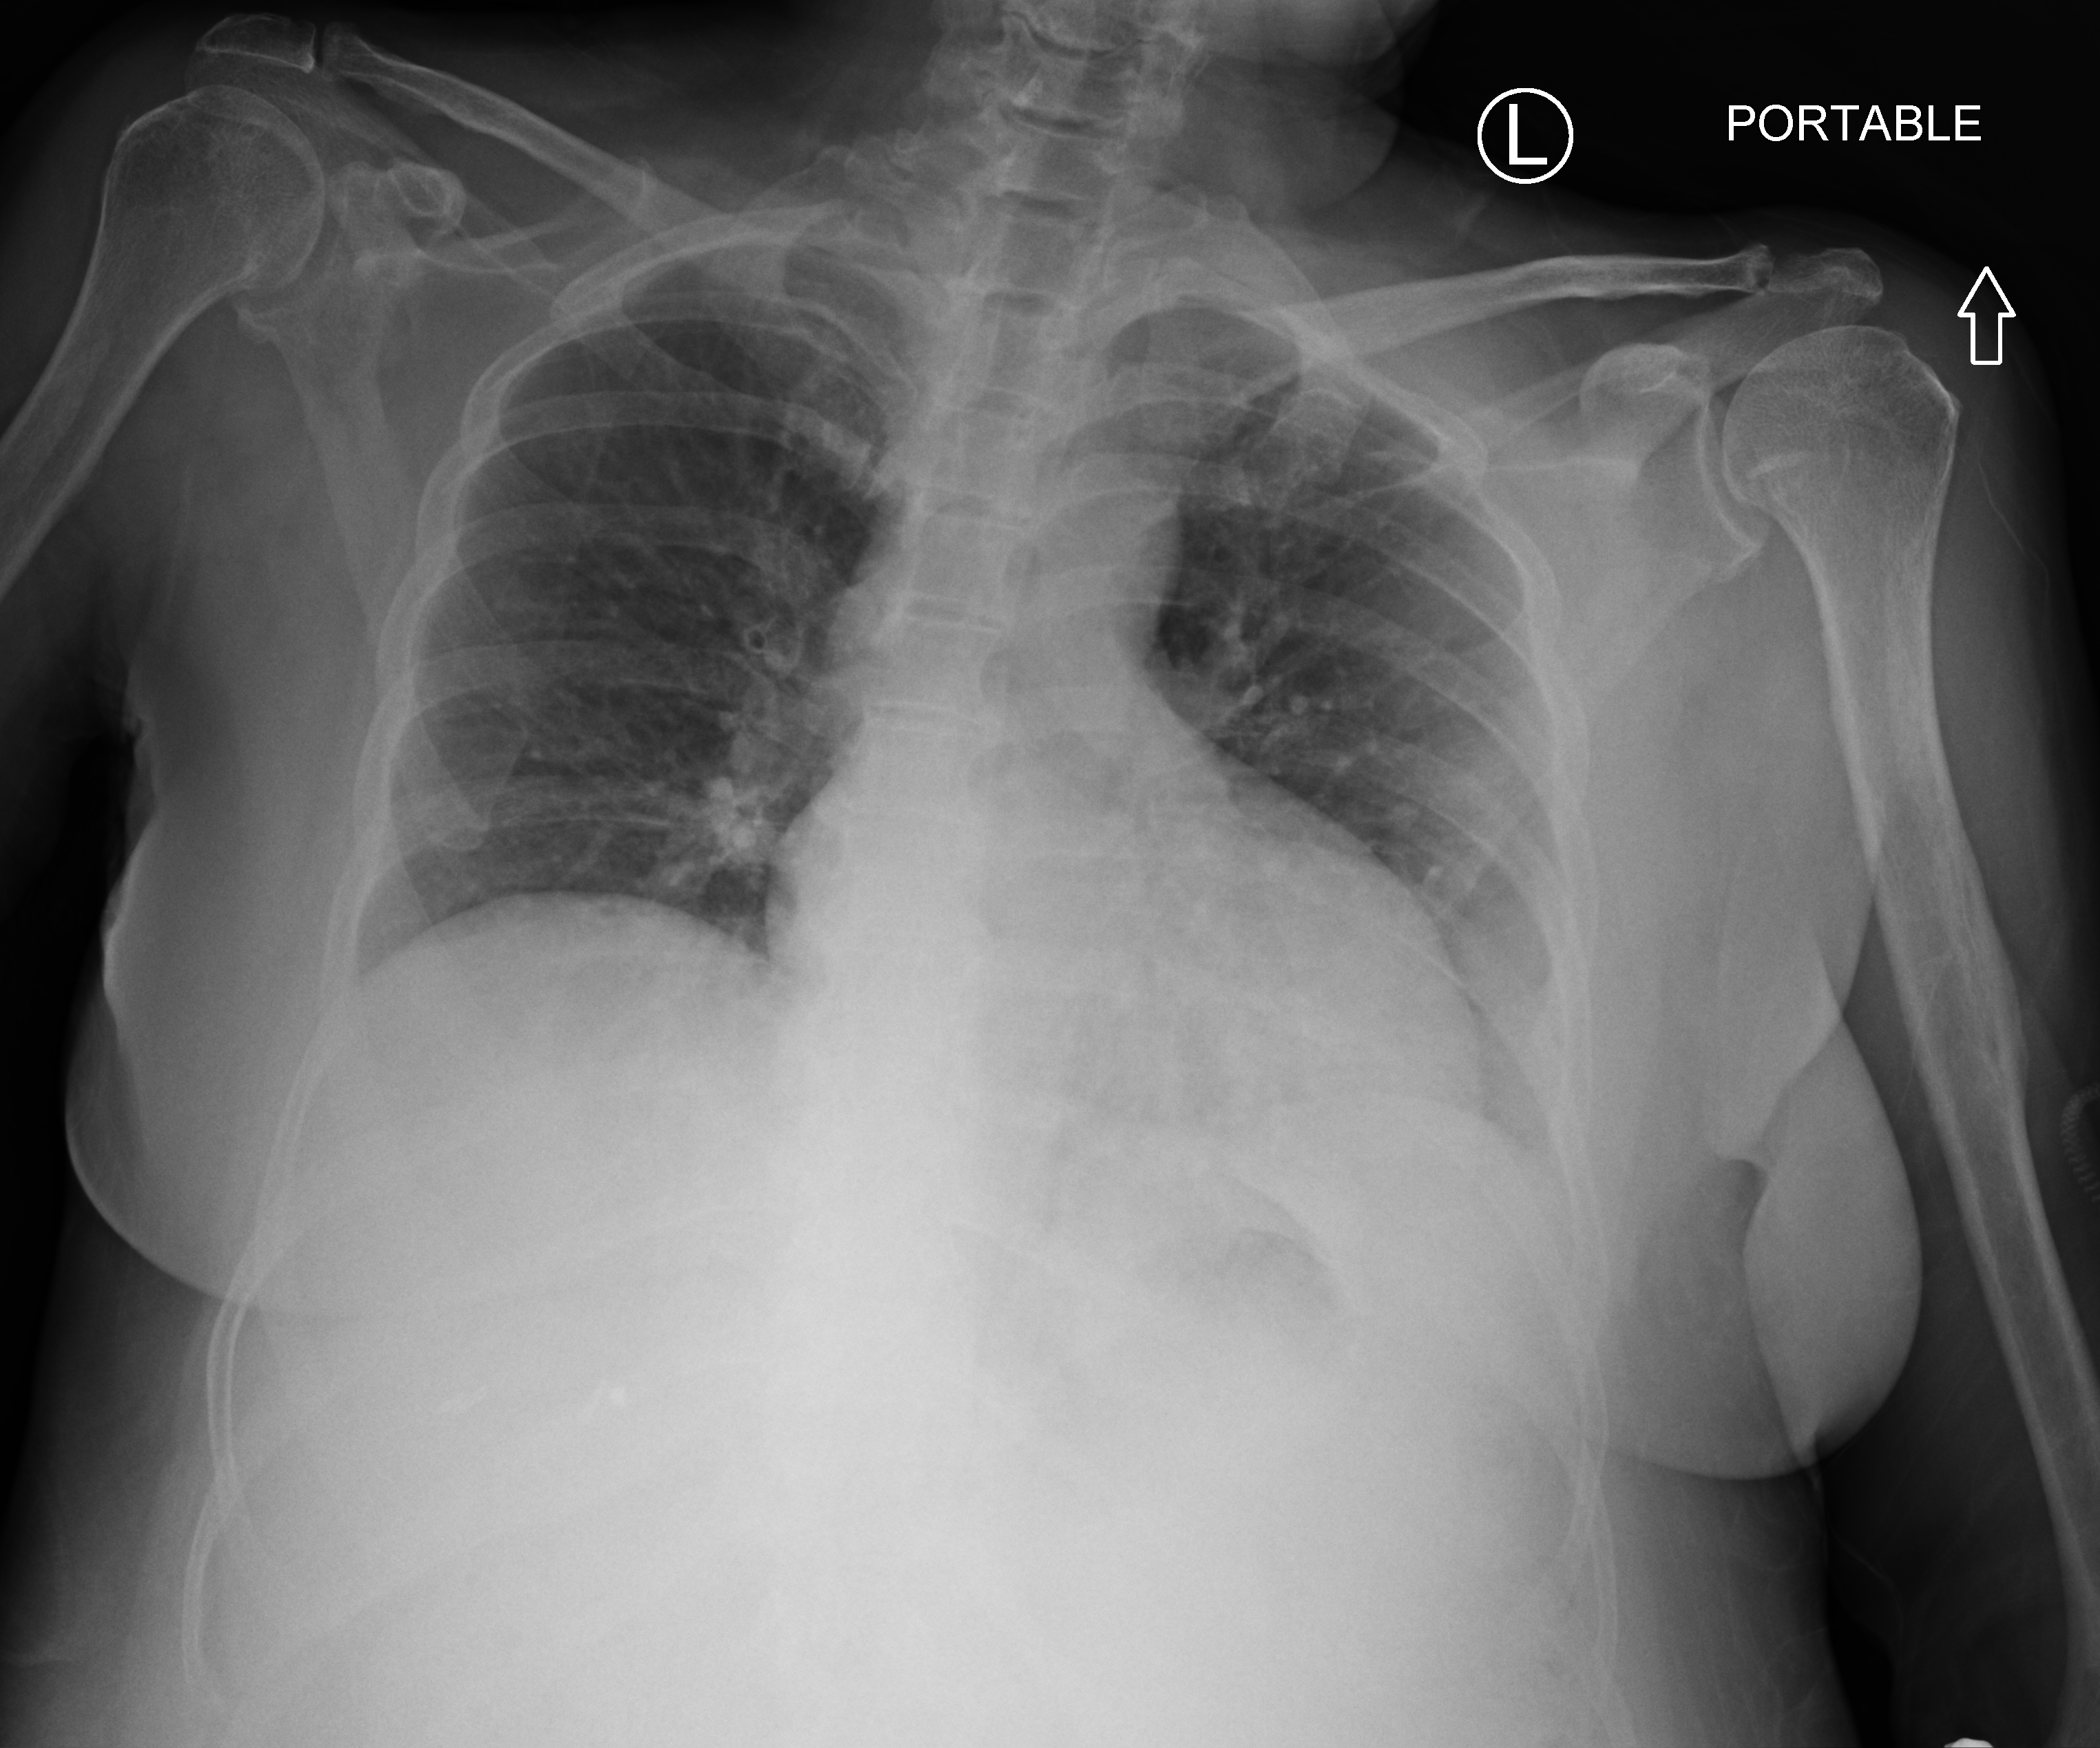
Portable chest radiograph, anteroposterior (AP) projection. Patient hospitalised with COVID-19; female, aged 18–59 years.
From the hospital-stay record, not from the radiograph (when in the stay this image was taken is not recorded): mechanically ventilated during this hospital stay: no.